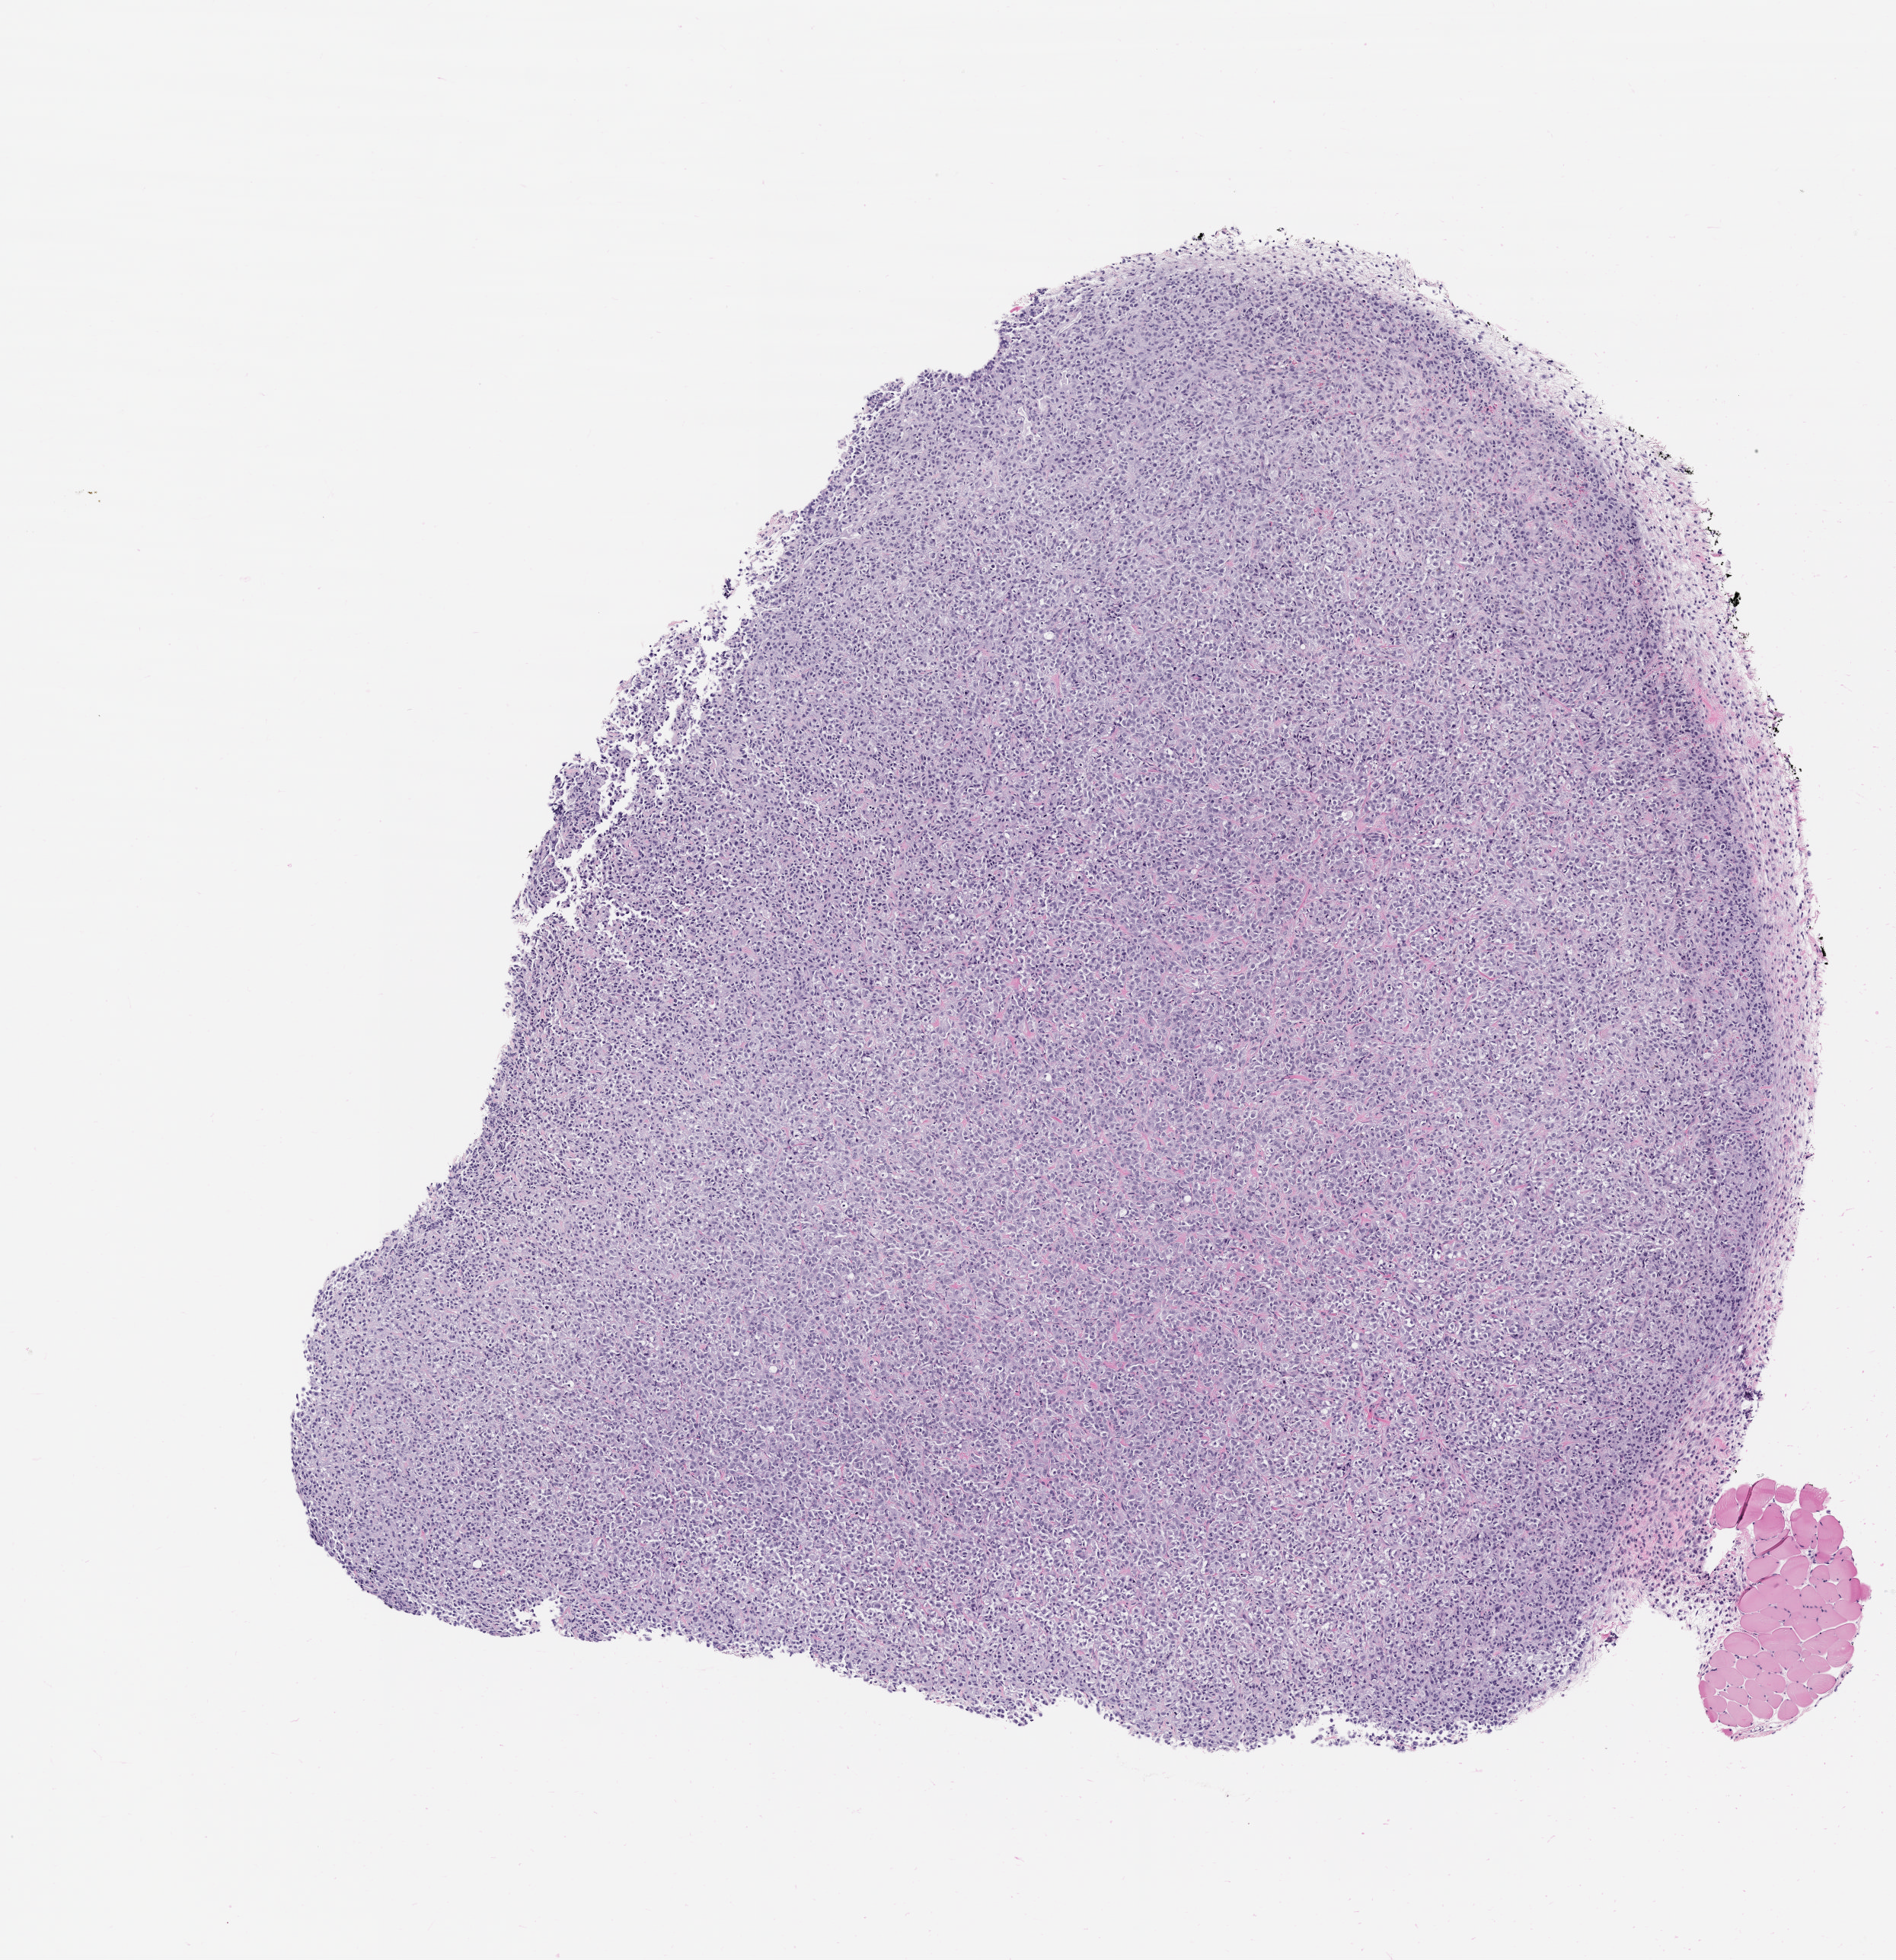
Whole-slide image, haematoxylin and eosin: patient-derived xenograft (human tumor grown in a mouse), passage 1, low-resolution overview of the scanned area, about 5.0 x 5.2 mm, formalin-fixed paraffin-embedded section, originating tumor site category: bone.
* originating patient diagnosis: Osteosarcoma